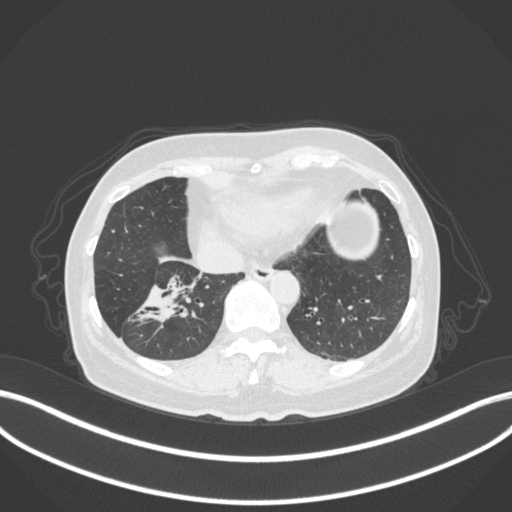
Chest CT, one axial slice. Position 112 of 429 along the scan axis. Reconstruction kernel B31f. Lung window (W 1500 / L -600 HU). 1 mm slice thickness. 512 × 512 image matrix, field of view 400 × 400 mm. Female patient, age 67 years. From the clinical record (not read from this slice): clinical TNM (as recorded): T1c N1 M0; histopathological grade: G2-3.
Annotated regions visible in this slice (bounding box drawn by a radiologist):
- lung tumour (recorded histology: adenocarcinoma): box from (x=129, y=270) to (x=212, y=335) px